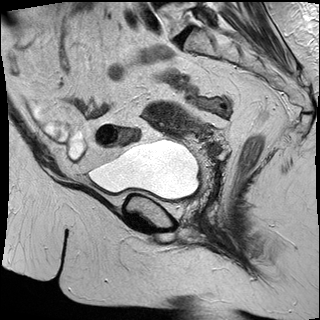
Pelvic MRI for cervical cancer, one sagittal slice; T2-weighted; 1.5 T; TE 87 ms, TR 3063.4 ms; 4 mm slice thickness; 320 × 320 image matrix. Female patient, age 53 years.
Outlined on this slice (manually delineated by an expert):
- uterus and cervix: bounding box (x1, y1, x2, y2) in pixels: (144, 101, 205, 138)